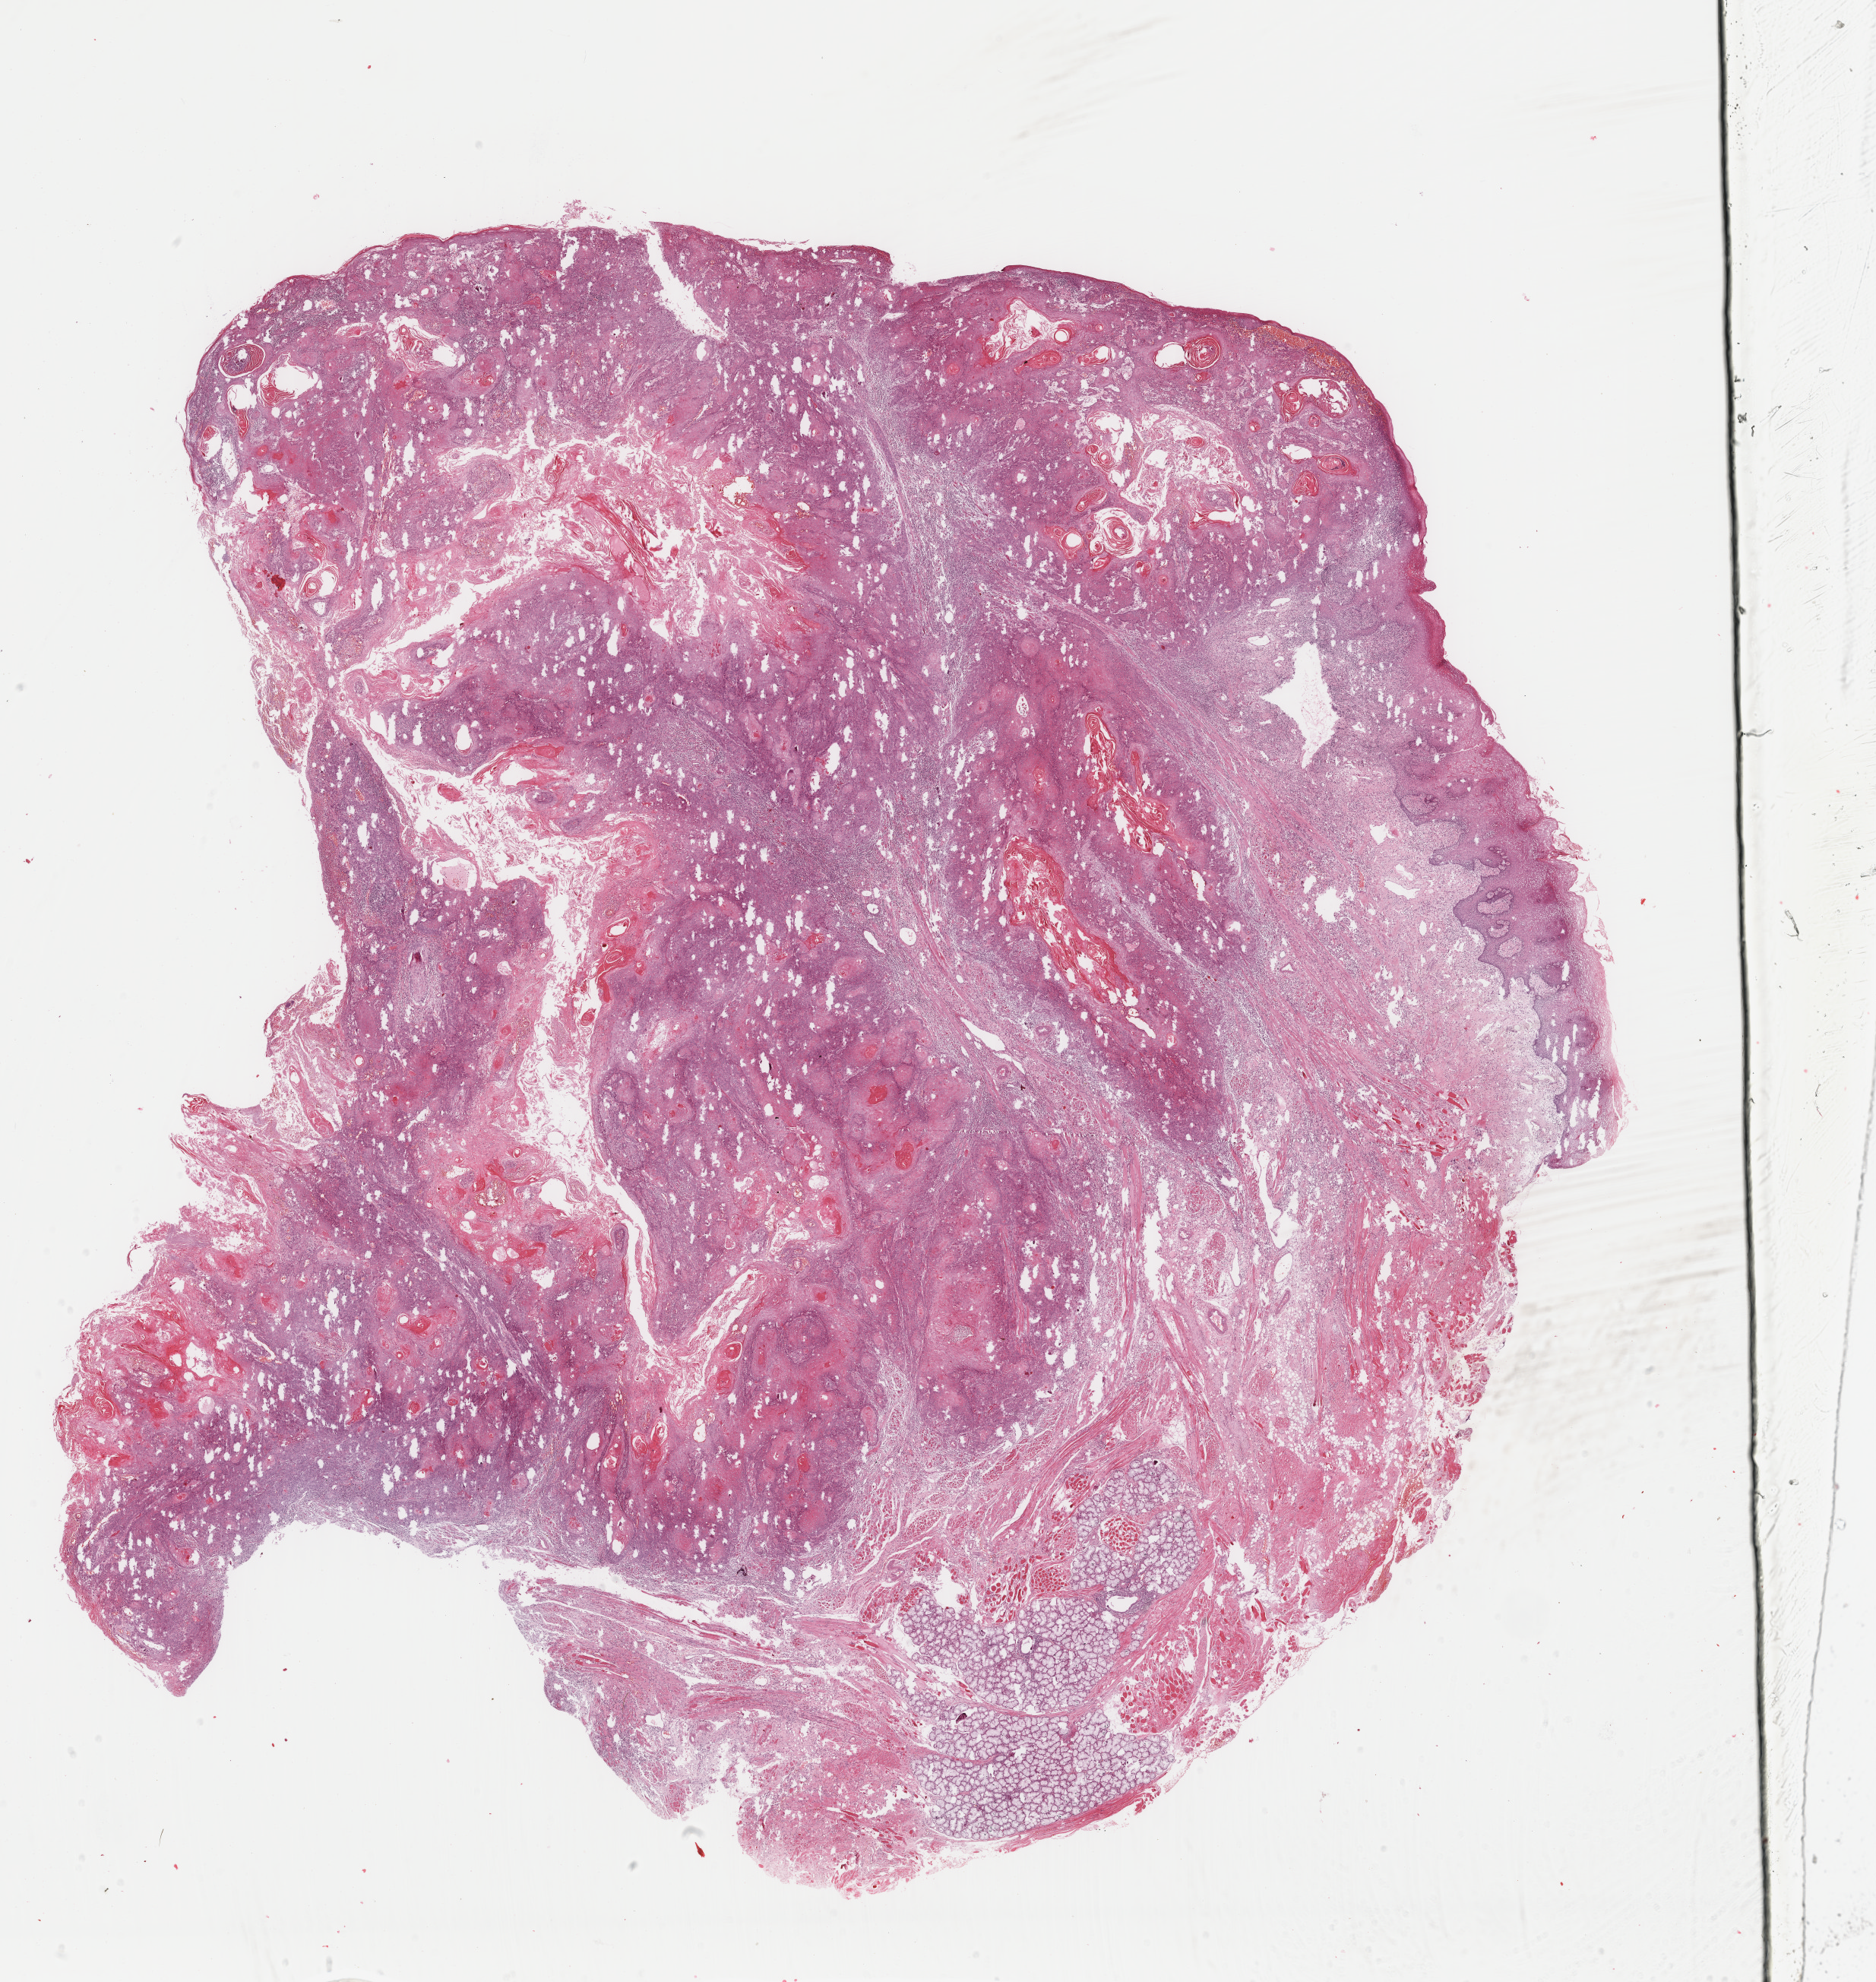
H&E-stained whole-slide image — a low-resolution overview of the entire scanned area, about 19.6 x 20.7 mm (slide scanned at 40x). Formalin-fixed paraffin-embedded (FFPE) diagnostic section. Sample: primary tumour, head and neck. Female, age 72 years at initial diagnosis. Histologic grade: G1 (well differentiated).
Diagnosis: Squamous cell carcinoma, NOS (tongue, NOS). Laterality: midline. AJCC pathologic stage: III.